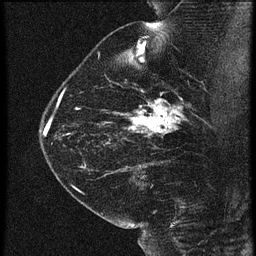
Breast MRI (dynamic contrast-enhanced), one sagittal slice; slice 42 of 60 in the series (ordered by position); 3 images stored at this slice position (order not interpretable as contrast timing); 1.5 T; TE 4.2 ms, TR 21.3 ms; 1.5 mm slice thickness; 256 × 256 image matrix, field of view 180 × 180 mm. Female patient, age 42 years. Case-level facts recorded for this patient, not image findings: setting: breast cancer imaged before/during neoadjuvant chemotherapy; receptor status: HER2-positive.
Outlined on this slice (semi-automatically segmented with operator editing):
- analysis volume of interest (the breast-tissue region the enhancement analysis was run in; not a lesion): bounding box <122,82,195,147> (left, top, right, bottom; pixels)
- tumour enhancement mask (voxels above the 90 % enhancement threshold inside the analysis volume of interest): <124,98,185,135>